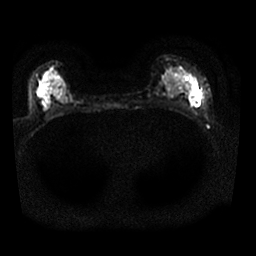
Breast MRI, one axial slice; position 16 of 25 along the scan axis; diffusion-weighted series; image 2 of 4 stored at this slice position (different b-values; order by instance number); 1.5 T; 256 × 256 image matrix. Female patient.
Annotated regions visible in this slice (expert manual segmentation):
- tumour on diffusion-weighted imaging: bounding box [x1, y1, x2, y2] px = [188, 88, 201, 108]